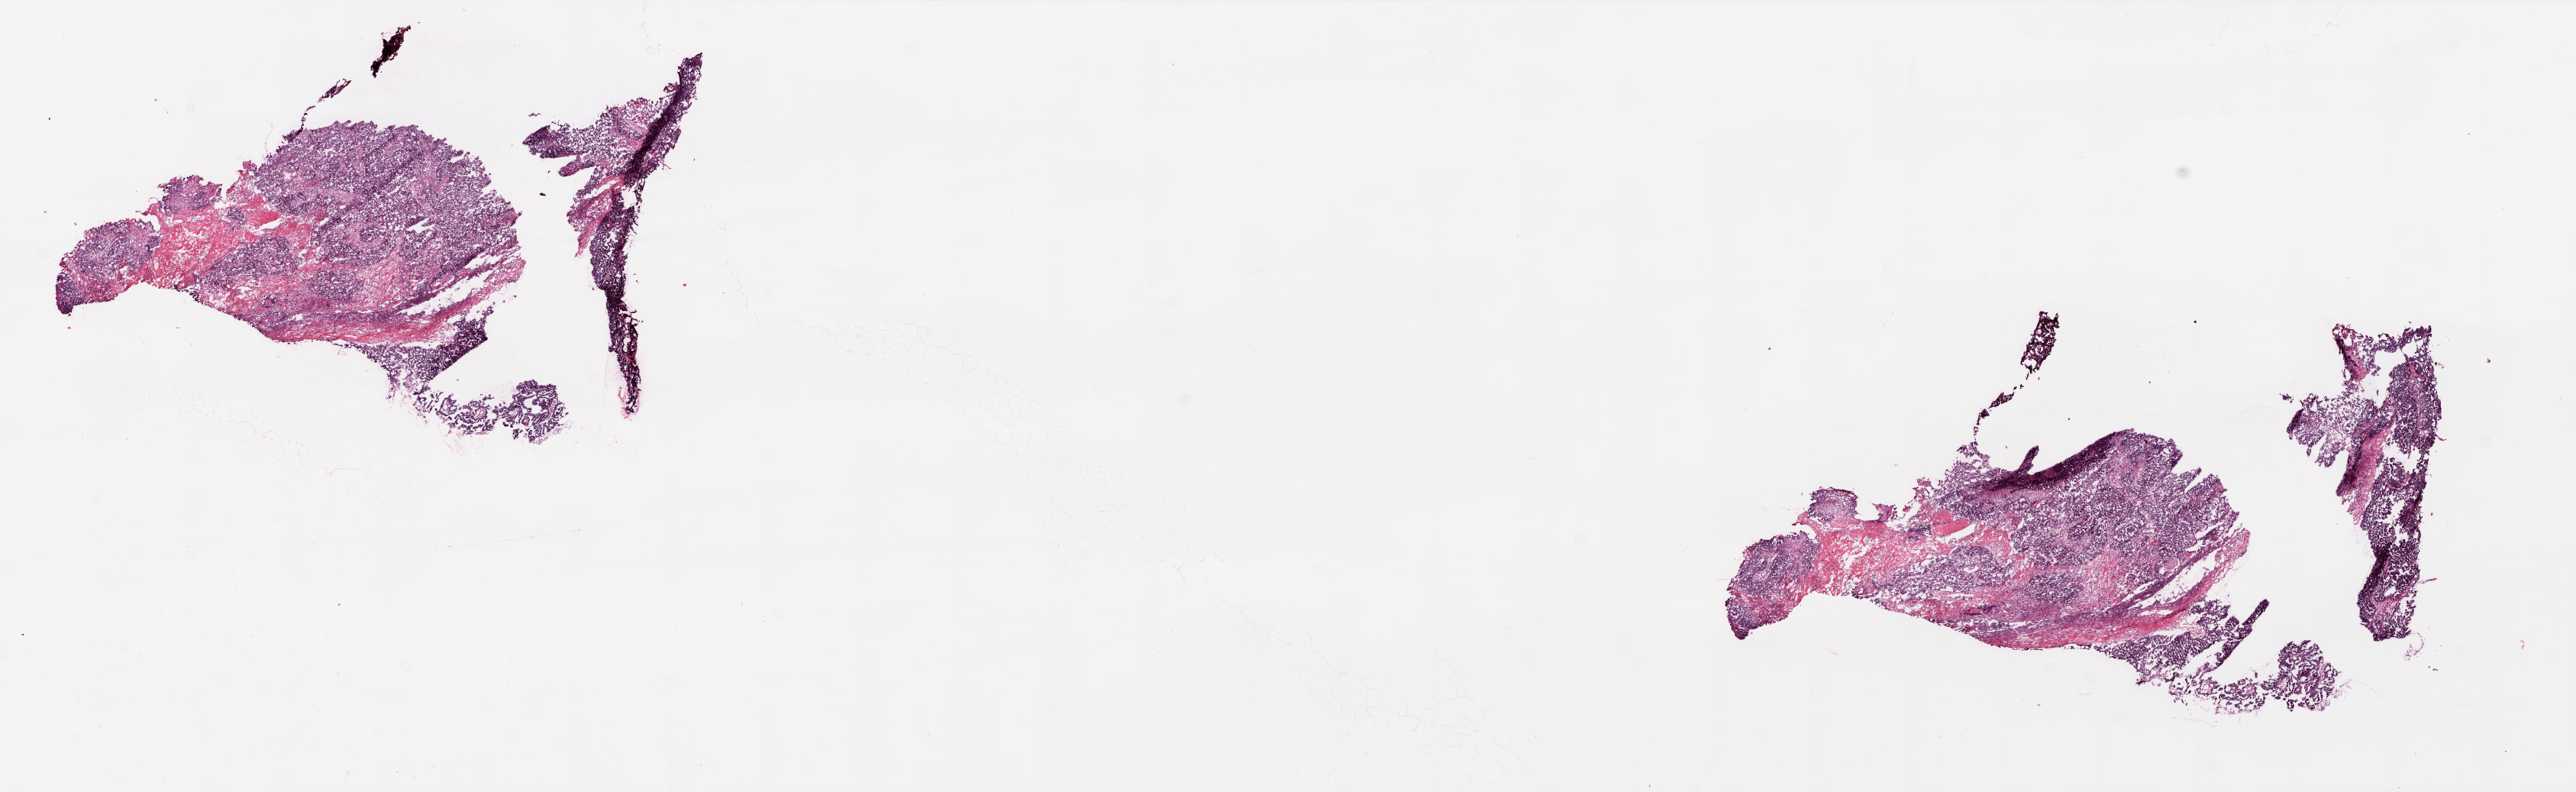
Digitized Hematoxylin and eosin (H&E) stained tissue section (whole slide) — a low-resolution overview of the entire scanned area, about 26.9 x 8.3 mm (acquisition: 20x scan); frozen section from the top of the tissue portion; primary tumour sample from the ovary. Patient: female, age at initial diagnosis 62 years. Histologic grade: G3 (poorly differentiated). Composition of this section per pathologist review: tumour cells 85%, tumour nuclei 99%, normal cells 0%, stromal cells 5%, necrosis 10%.
FIGO stage: IIC. Diagnosis: Serous cystadenocarcinoma, NOS.